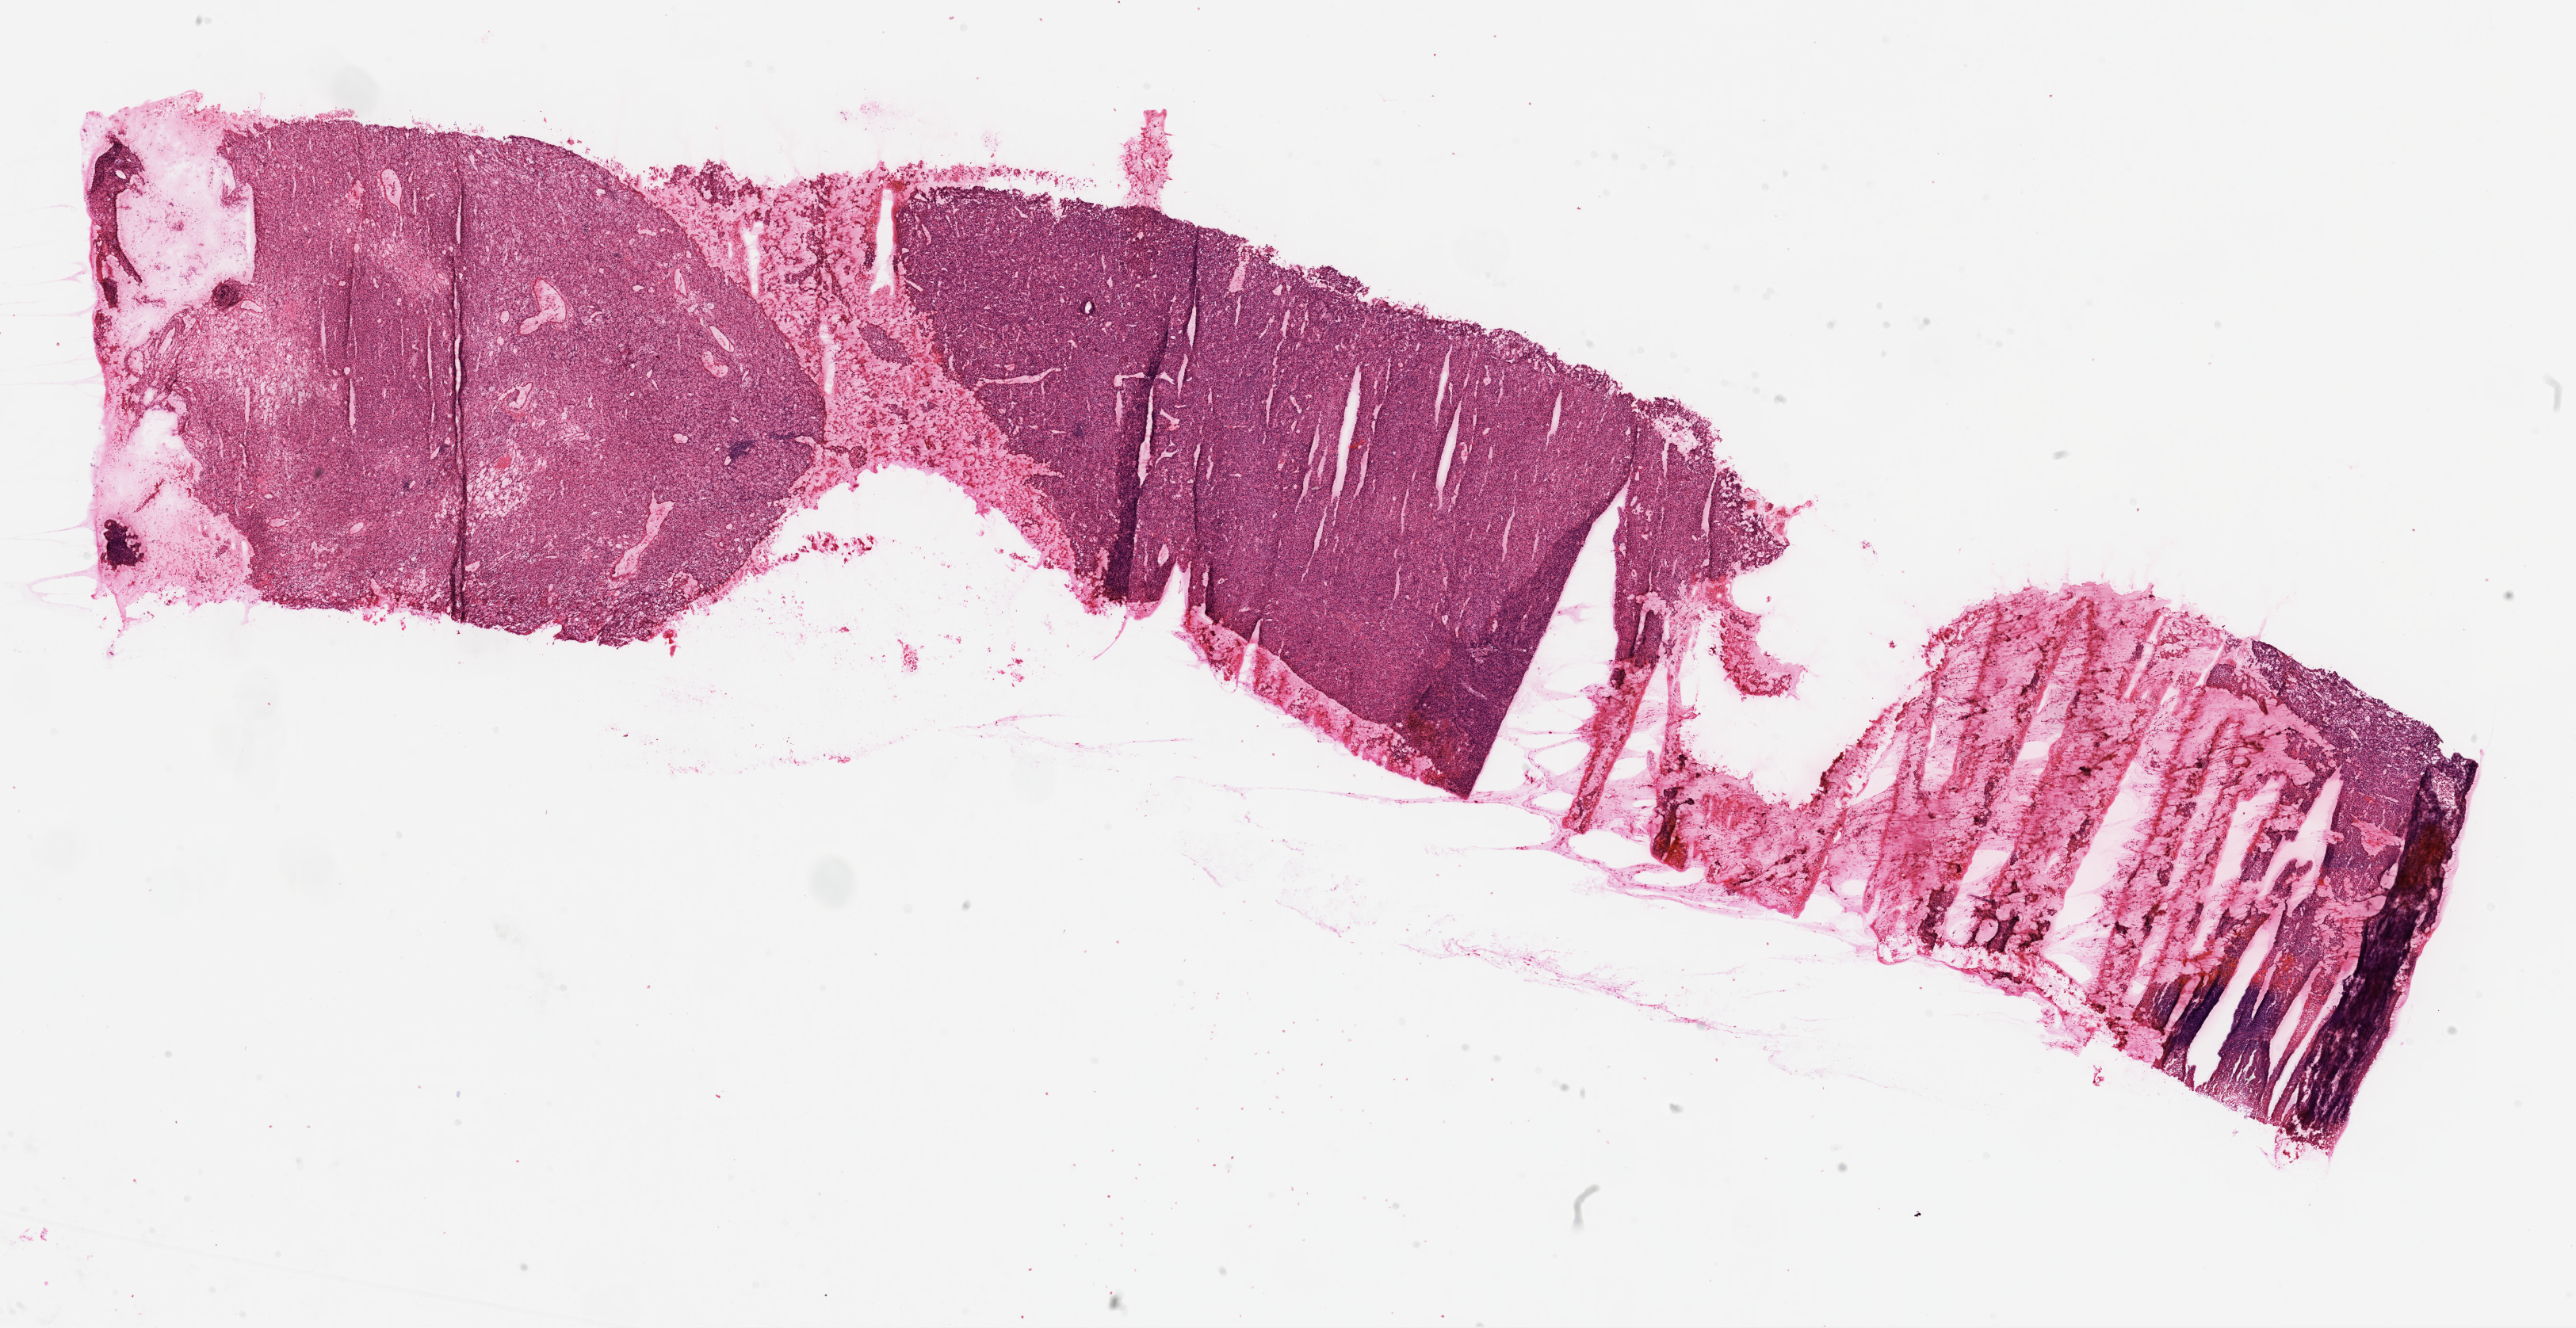
H&E whole-slide image, shown as a low-resolution overview of the whole scanned area (about 26.1 x 13.4 mm), frozen section from the top of the tissue portion, sample: primary tumour, kidney. Patient: male, age at initial diagnosis 63 years. Histologic grade: G4 (undifferentiated). Composition of this section per pathologist review: tumour cells 85%, tumour nuclei 85%, normal cells 0%, stromal cells 15%, necrosis 0%.
- AJCC pathologic stage: IV
- TNM: T3a NX M1
- laterality: left
- pathologic diagnosis: Clear cell adenocarcinoma, NOS